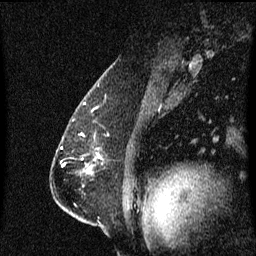
Breast MRI (dynamic contrast-enhanced), one sagittal slice. Dynamic contrast-enhanced series, image 2 of 3 at this slice position (ordered by acquisition). 1.5 T. TE 4.2 ms, TR 8.4 ms. 2 mm slice thickness. 256 × 256 image matrix, field of view 200 × 200 mm. Female patient, age 57 years. From the clinical record (not read from this slice): setting: breast cancer imaged before/during neoadjuvant chemotherapy; receptor status: HR-positive, HER2-negative.
Annotated regions visible in this slice (semi-automatically segmented with operator editing):
- analysis volume of interest (the breast-tissue region the enhancement analysis was run in; not a lesion): box from (x=86, y=154) to (x=101, y=175) px
- tumour enhancement mask (voxels above the 70 % enhancement threshold inside the analysis volume of interest): (x=97, y=154)–(x=100, y=159)